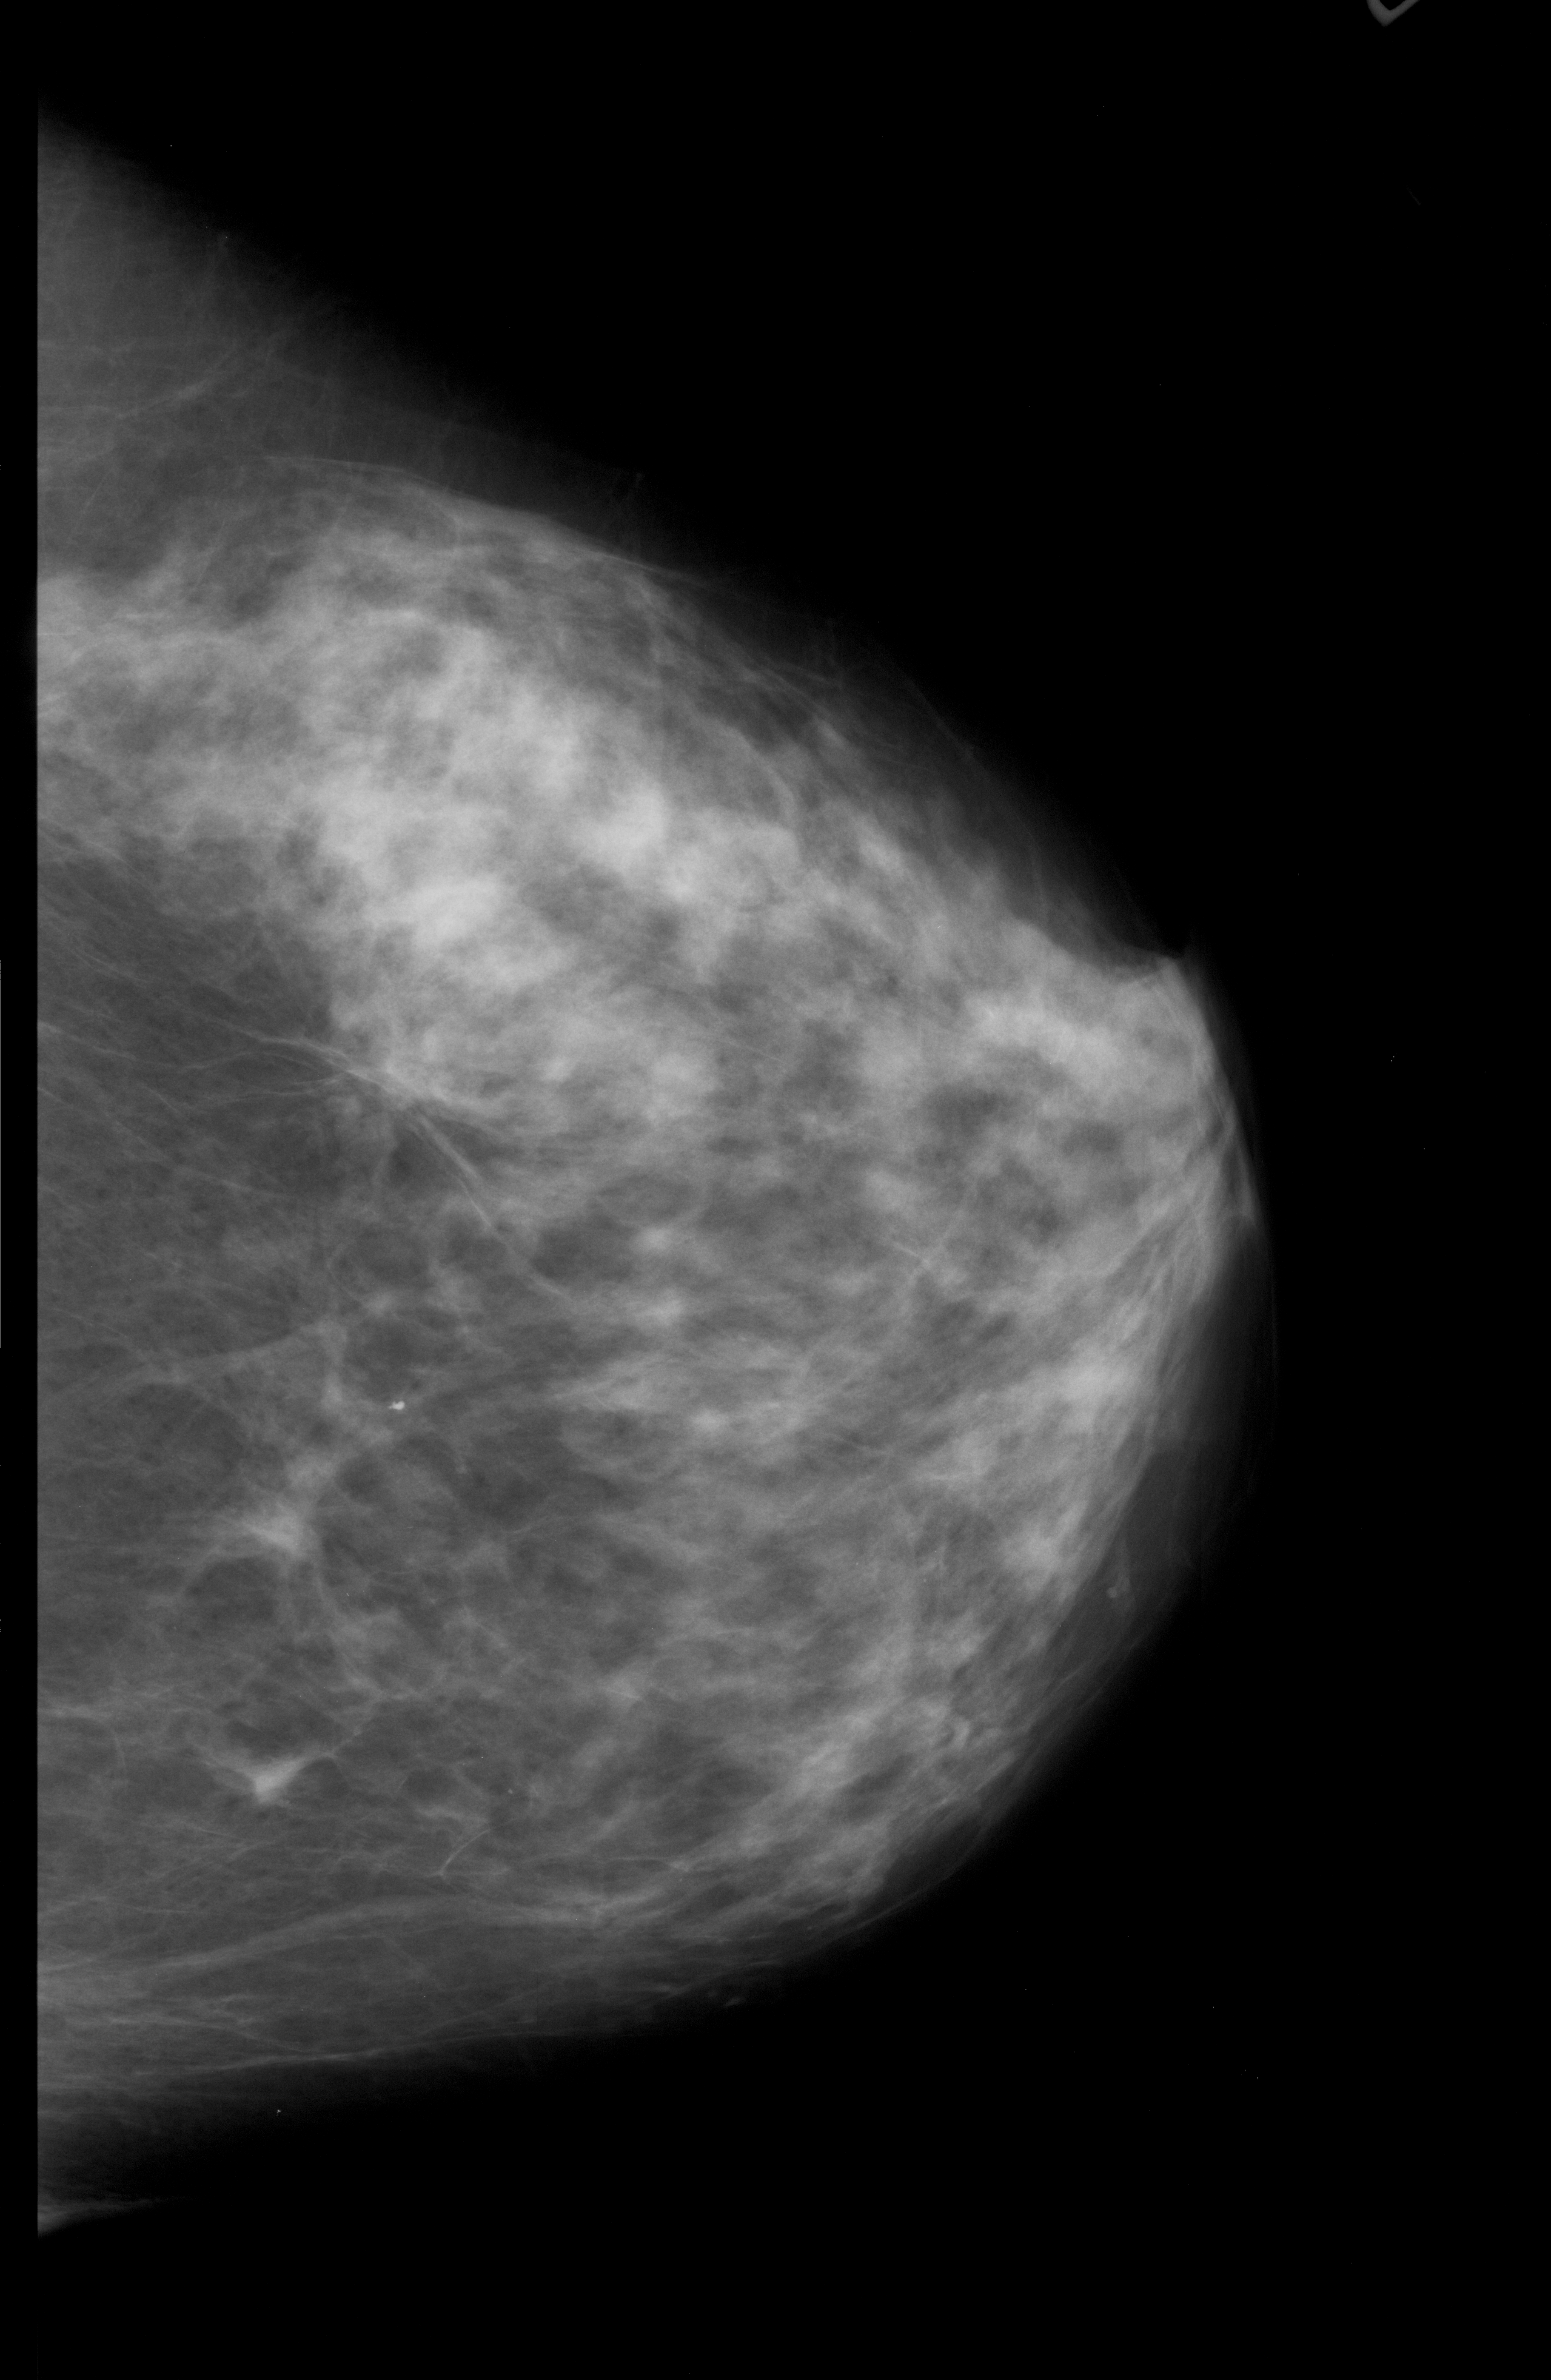
Mammogram (digitized film), right breast, CC view, BI-RADS breast density category 3 (scale 1–4).
Mass, shape architectural distortion, margins spiculated; BI-RADS assessment category 5; subtlety rating 1 on a 1 (subtle) to 5 (obvious) scale; pathology (as recorded): malignant.